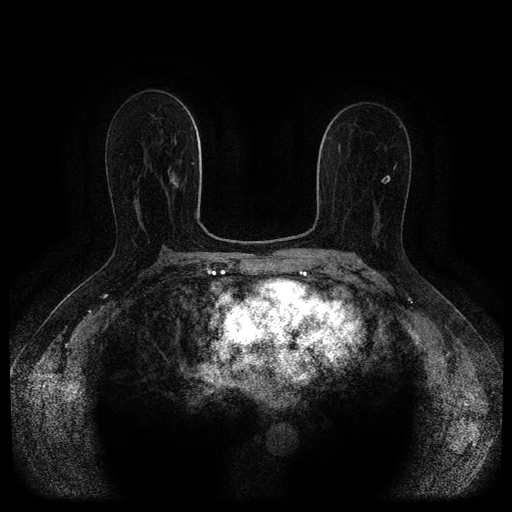
Breast MRI (dynamic contrast-enhanced, multi-phase), one axial slice. Position 60 of 116 along the scan axis. Dynamic contrast-enhanced series, time point 2 of 5 at this slice position (early post-contrast). 1.5 T. TE 2.7 ms, TR 5.4 ms. 512 × 512 image matrix. Female patient, age 71 years.
Structures marked on this image (semi-automatic segmentation, software-assisted and operator-edited):
- breast lesion (labelled 'tumour' in the annotation; benign lesions carry a separate 'benign' label): bounding box (x1, y1, x2, y2) in pixels: (170, 174, 179, 187)